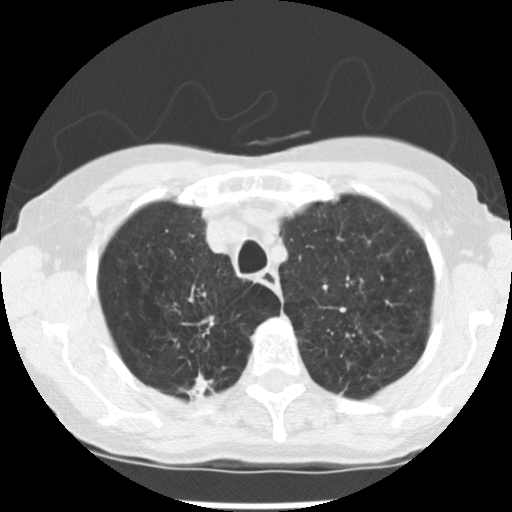
Low-dose screening chest CT, axial slice, baseline screening round, lung window (W 1500 / L -600 HU), 2.5 mm slice thickness, 120 kVp, slice 45 of 265 in the series, 512 × 512 image matrix, field of view 300 × 300 mm. Female, age 72 years at enrolment.
- Expert-annotated lung lesion, bounding box (x1, y1, x2, y2) in pixels: (182, 365, 230, 406).
- The screening reader recorded 3 non-calcified nodules or masses ≥4 mm on this exam (right upper lobe, left upper lobe, left lower lobe); which of them this box marks is not recorded.